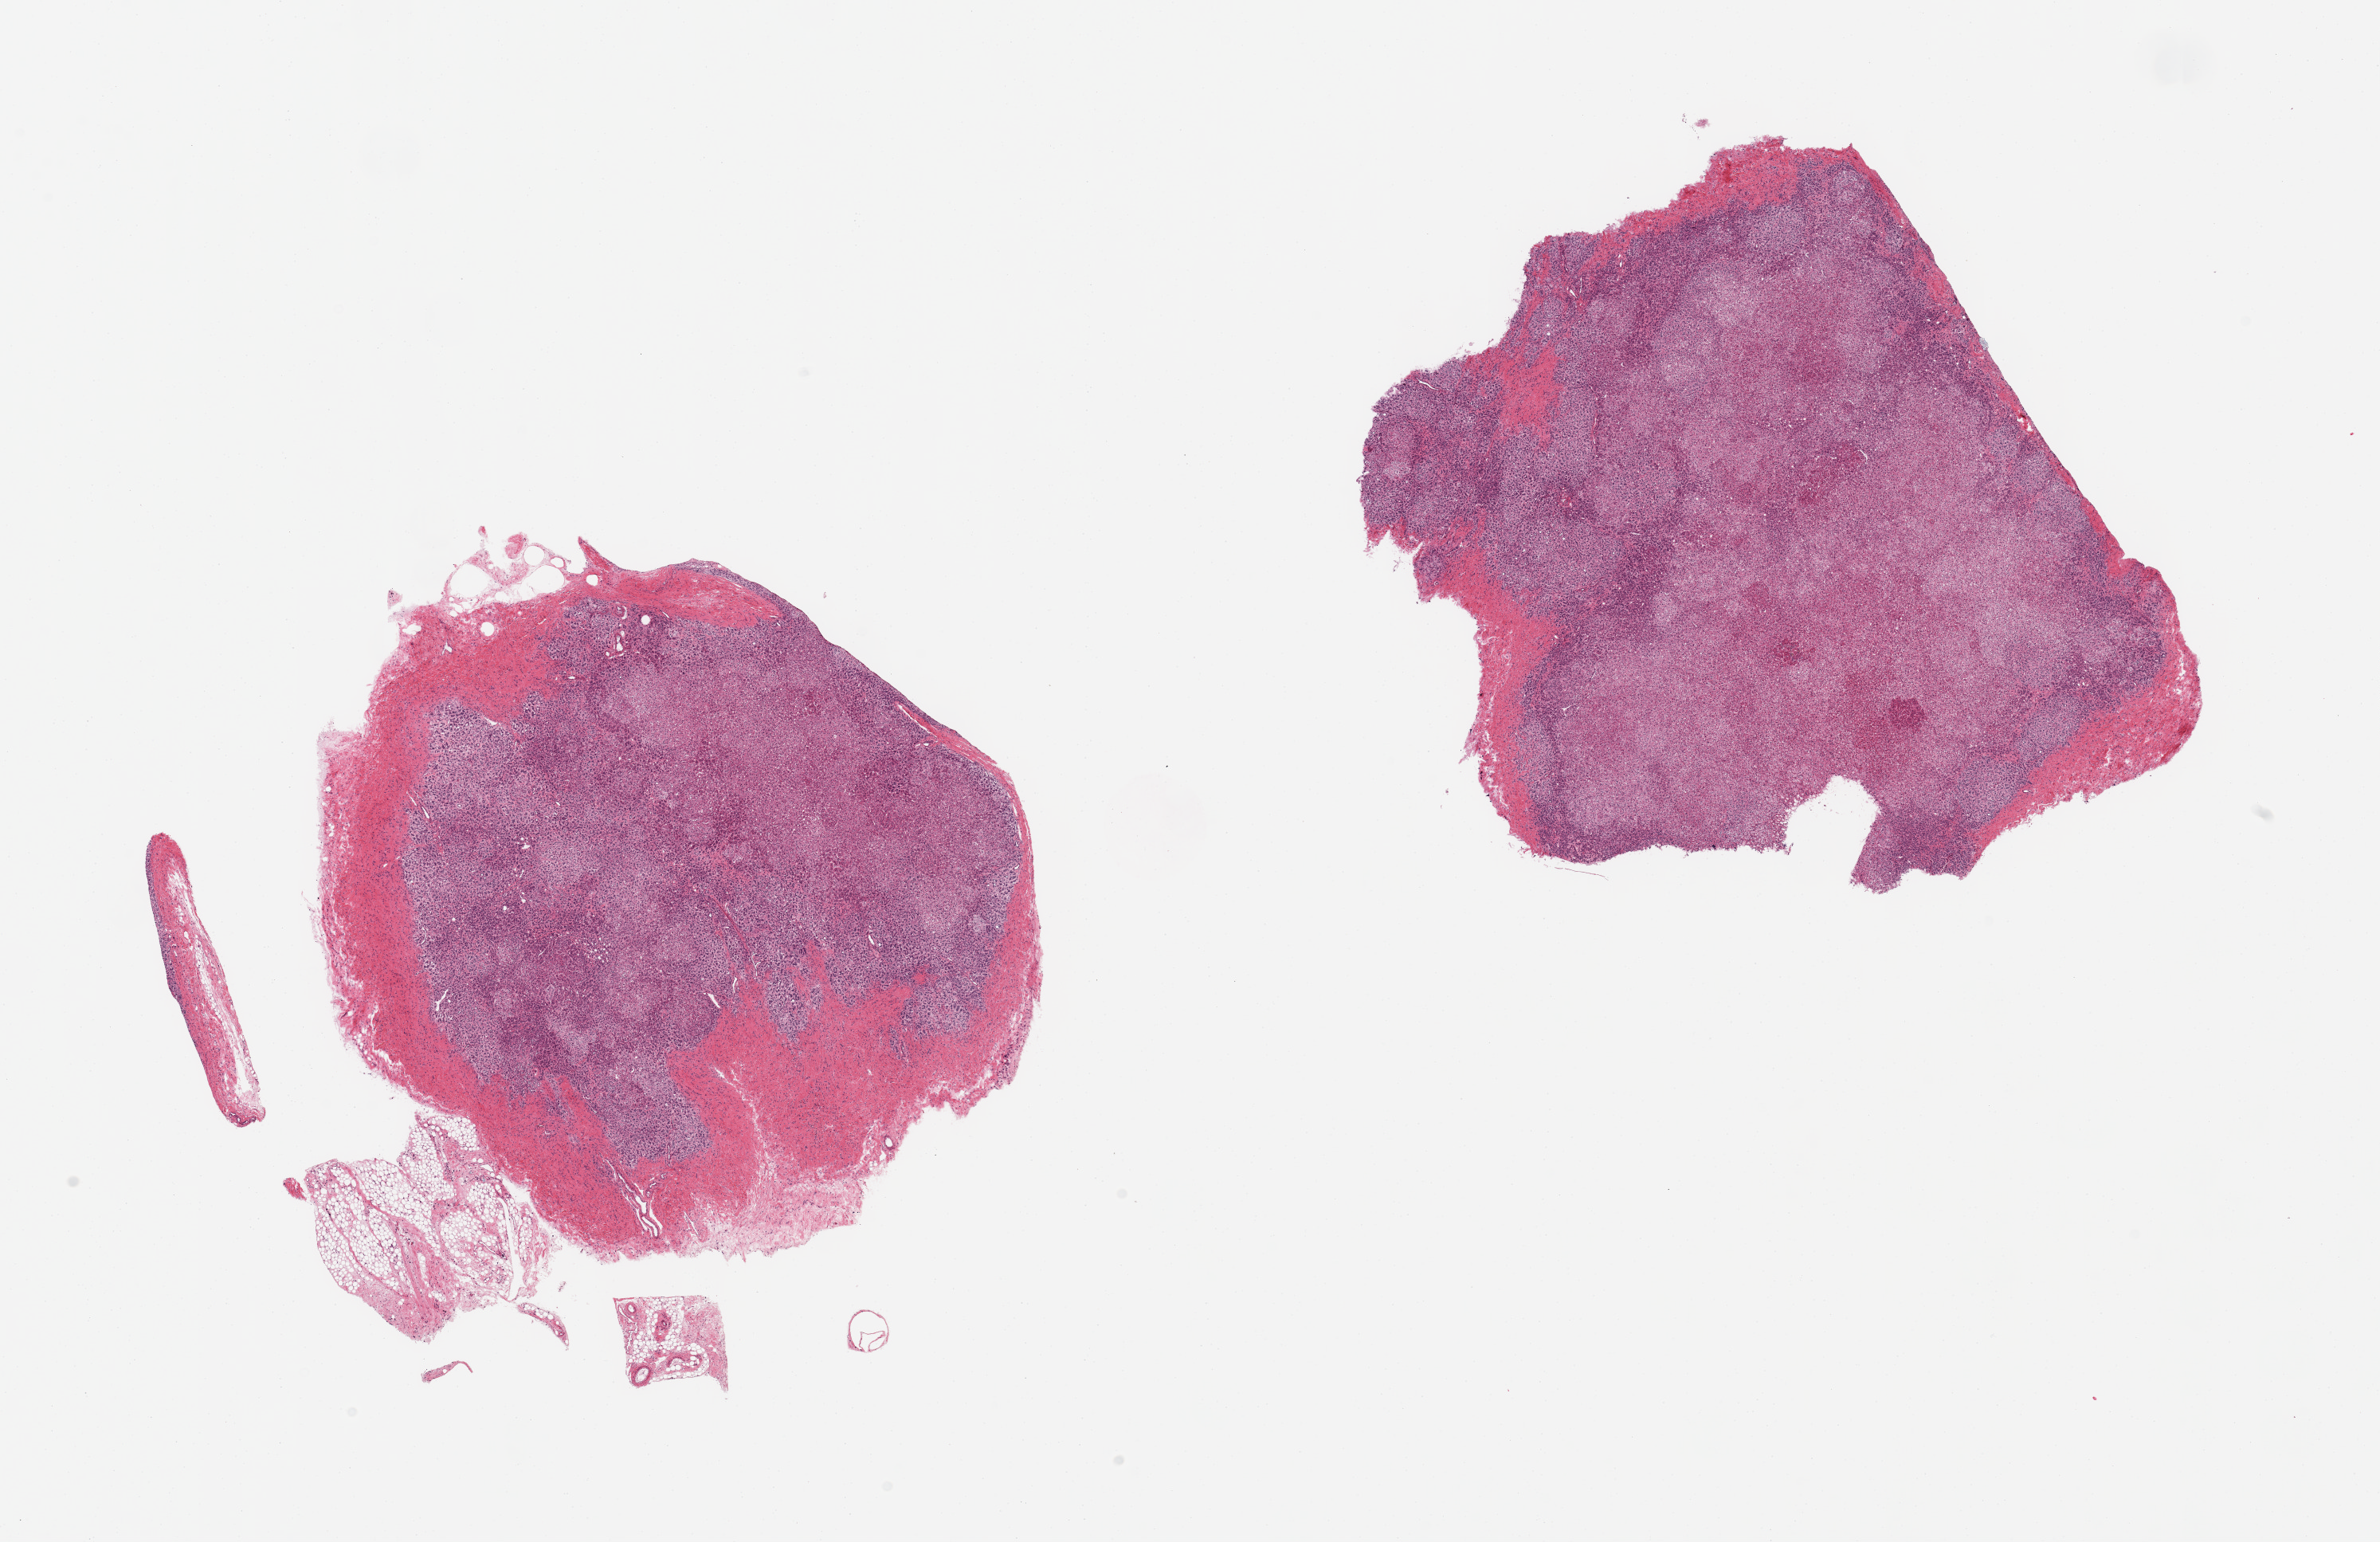
Hematoxylin and eosin (H&E) whole-slide image, brightfield, low-resolution overview of the scanned area, about 23.6 x 15.3 mm; PAXgene-fixed, paraffin-embedded tissue; sampled site (target tissue): adrenal gland; tissue donor sample. Donor sex: female.
Pathologist's review note for this sample: 2 pieces all cortex, rim of fibrous tissue up to ~0.5mm.